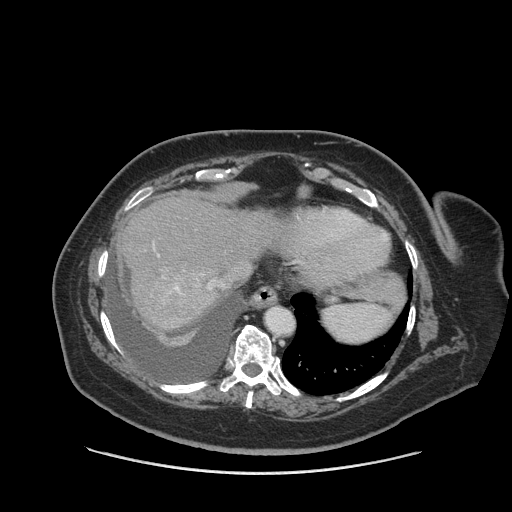
Contrast-enhanced abdominal CT (liver protocol), one axial slice. Slice 72 of 91 in the series (ordered by position). Soft-tissue window (W 400 / L 40 HU). 2.5 mm slice thickness. 512 × 512 image matrix, field of view 420 × 420 mm. Case-level facts recorded for this patient, not image findings: diagnosis: hepatocellular carcinoma (patient treated with transarterial chemoembolisation; whether this scan precedes or follows treatment is not stated here); TNM stage (as recorded): Stage-I; Child-Pugh class: A; tumour differentiation: well differentiated.
Outlined on this slice (semi-automatically segmented with operator editing):
- abdominal aorta: bounding box <266,308,293,335> (left, top, right, bottom; pixels)
- liver parenchyma outside the tumour (the mass and vessels are separate outlines, so this box may not span the whole liver): <118,192,284,330>
- liver vessels: <158,255,211,293>